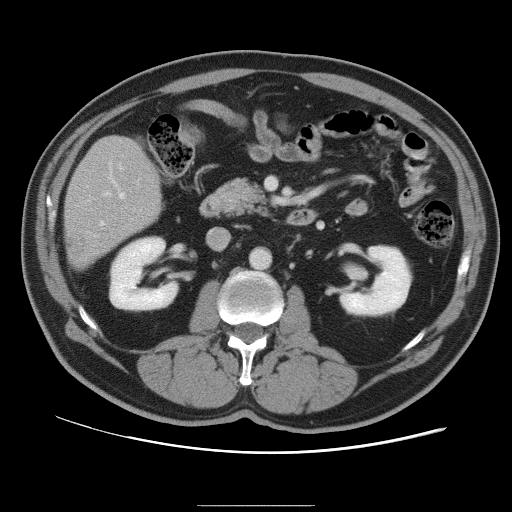
Contrast-enhanced abdominal CT, one axial slice; slice 38 of 105 in the series (ordered by position); soft-tissue window (W 400 / L 40 HU); 5 mm slice thickness; 512 × 512 image matrix, field of view 399 × 399 mm. Male patient, age 64 years. Case-level facts recorded for this patient, not image findings: diagnosis: colorectal cancer liver metastases, imaged before liver resection; multiple liver metastases: yes; largest metastasis: 3 cm; chemotherapy before resection: yes.
Structures marked on this image (outlined manually by an expert reader):
- hepatic veins: box from (x=100, y=193) to (x=125, y=226) px
- liver: (x=65, y=137)–(x=162, y=268)
- planned liver remnant (the part of the liver to remain after resection): (x=66, y=137)–(x=162, y=242)
- portal vein (with intrahepatic branches): (x=103, y=164)–(x=123, y=196)
- liver metastasis: (x=69, y=230)–(x=86, y=258)